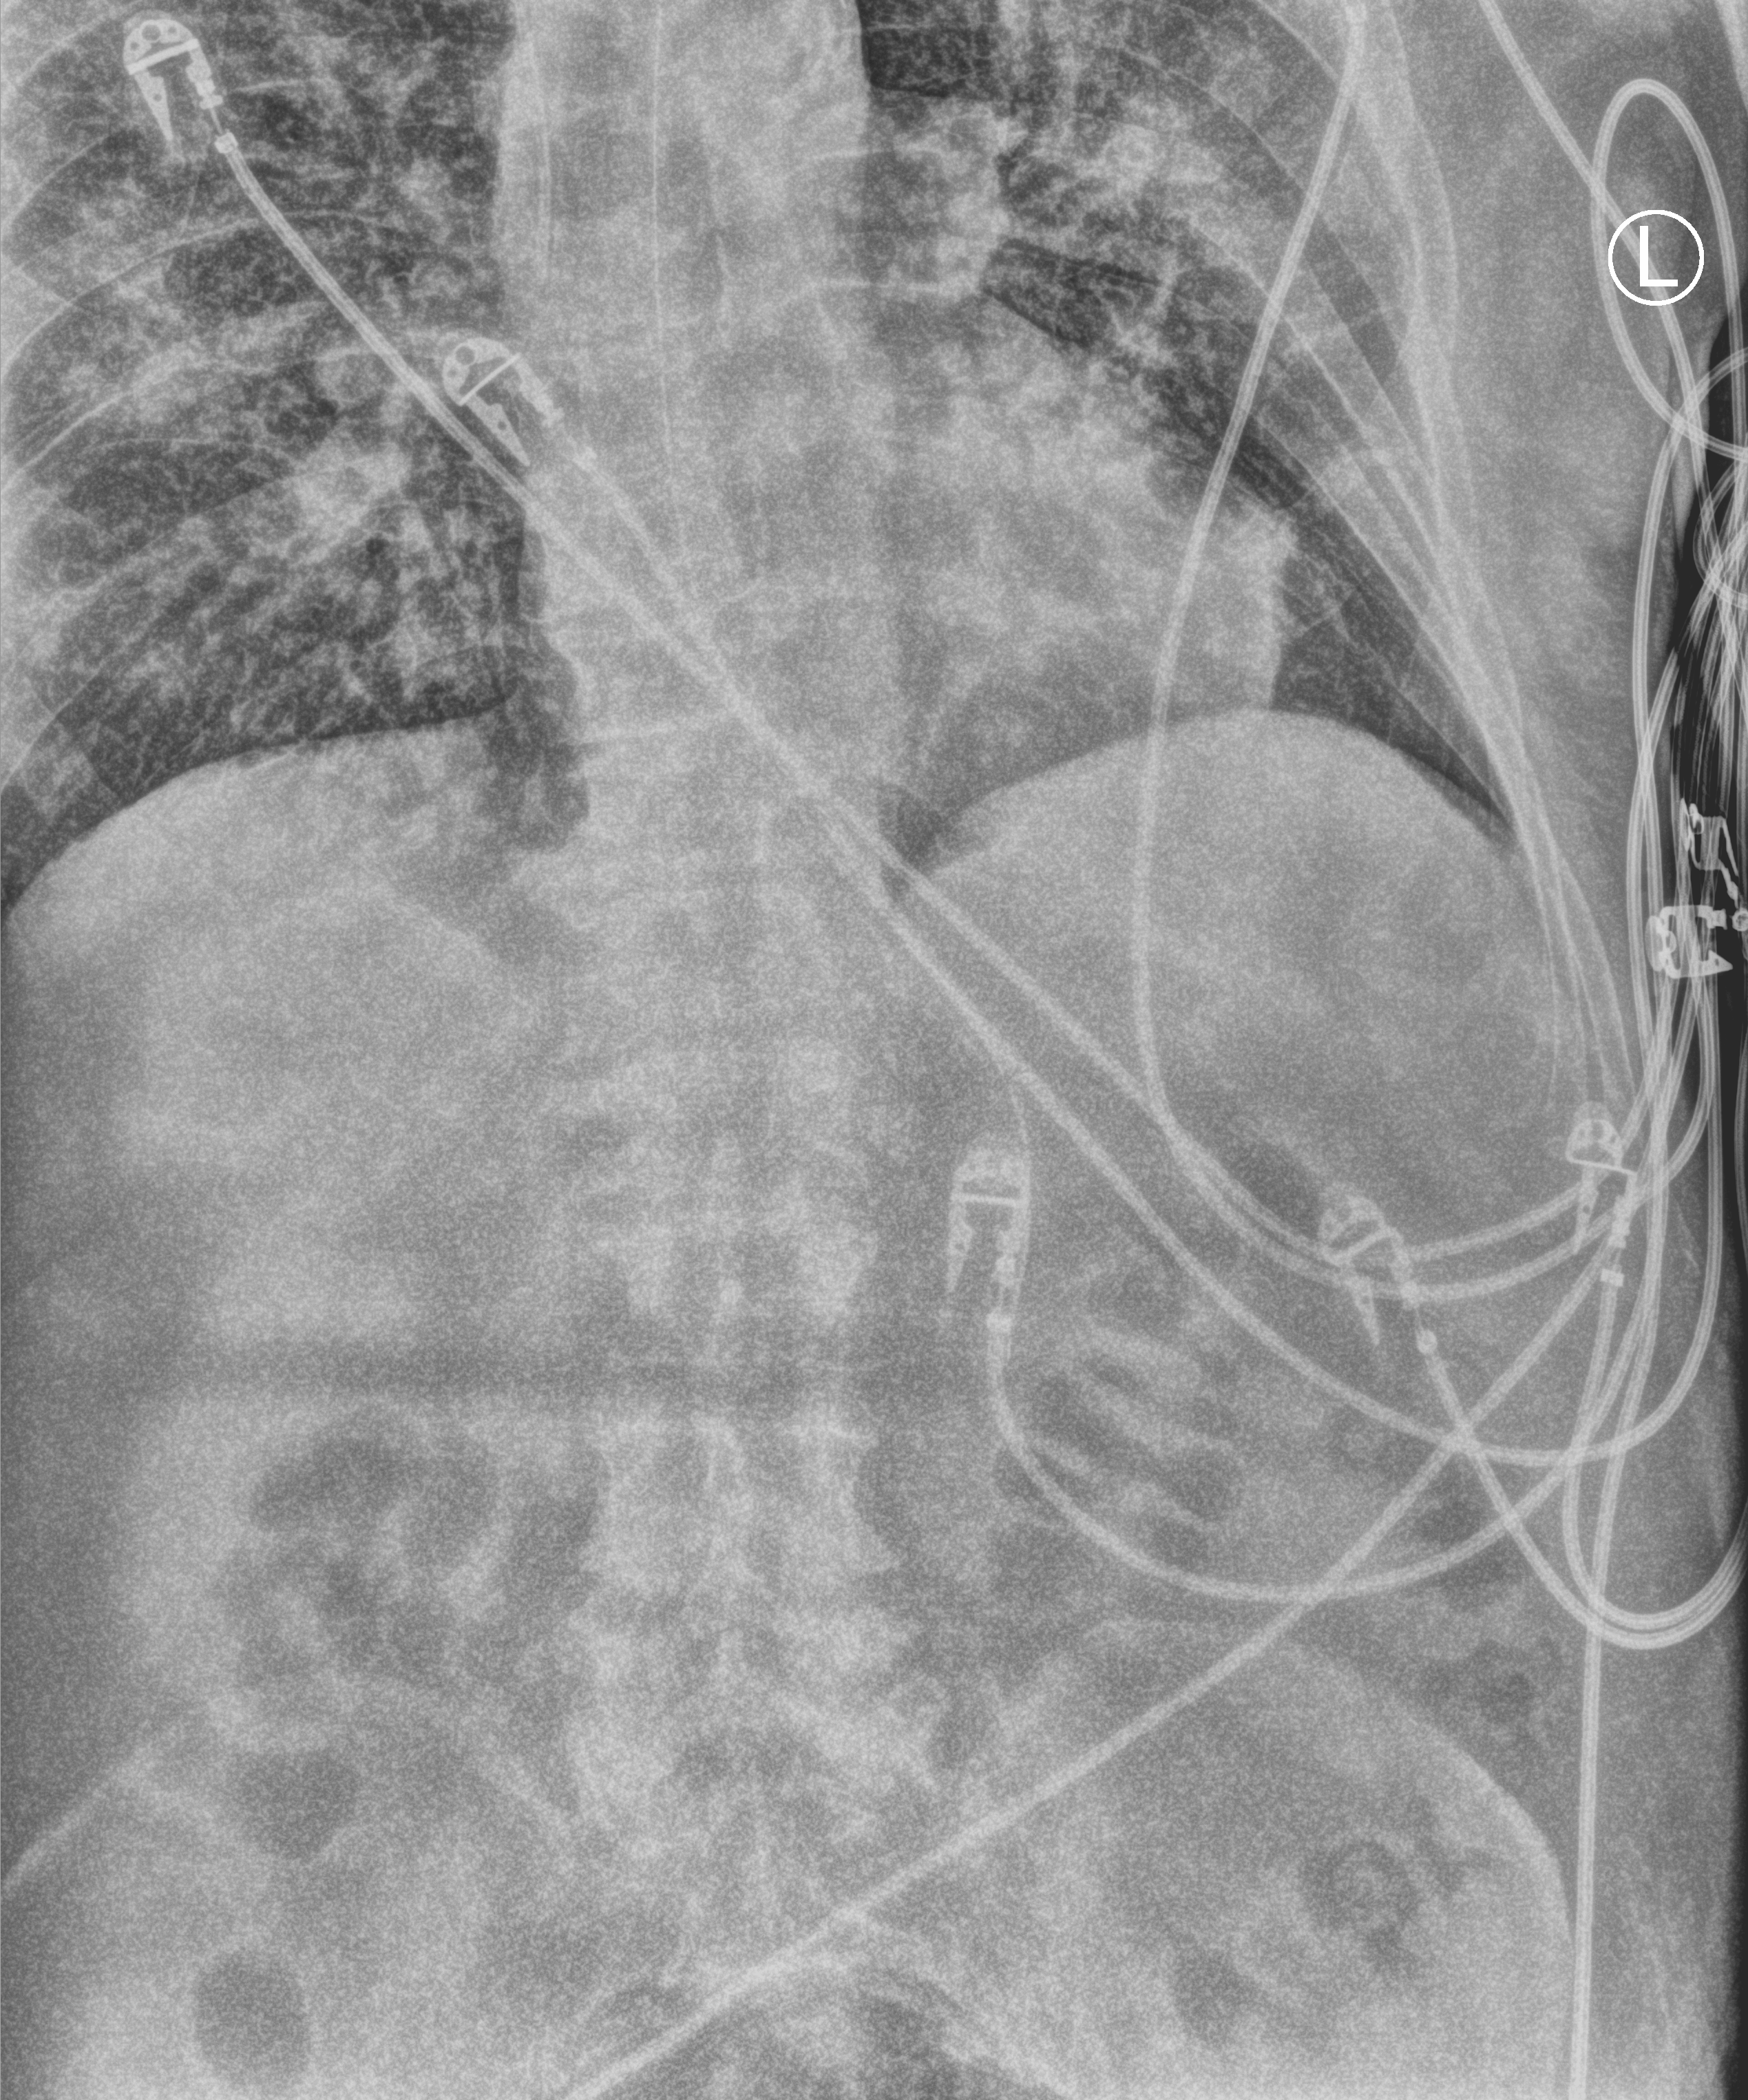
Chest X-ray (portable); anteroposterior (AP) projection. Patient hospitalised with COVID-19; male, aged 75–90 years.
Hospital-stay facts (about this admission, not read from this image; timing relative to this image not recorded): mechanically ventilated during this hospital stay: yes; admitted to intensive care during this hospital stay: yes; length of hospital stay: 26 days.